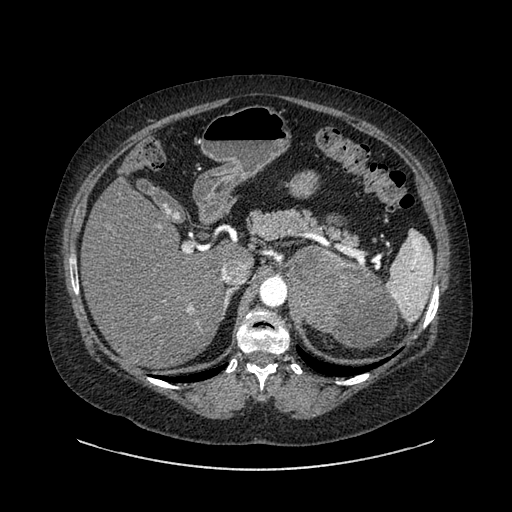
Contrast-enhanced abdominal CT, one axial slice. Position 593 of 769 along the scan axis. 120 kVp. Intravenous contrast given. Soft-tissue window (W 400 / L 40 HU). 0.62 mm slice thickness. 512 × 512 image matrix, field of view 460 × 460 mm. Patient: female, 61 years. From the clinical record (not read from this slice): diagnosis: adrenocortical carcinoma; tumour side: left adrenal; tumour size at pathology: 13 cm; Ki-67 index: 79 %; stage (as recorded): 2.
Annotated regions visible in this slice (semi-automatically segmented with operator editing):
- mass: bounding box [x1, y1, x2, y2] px = [285, 249, 394, 347]